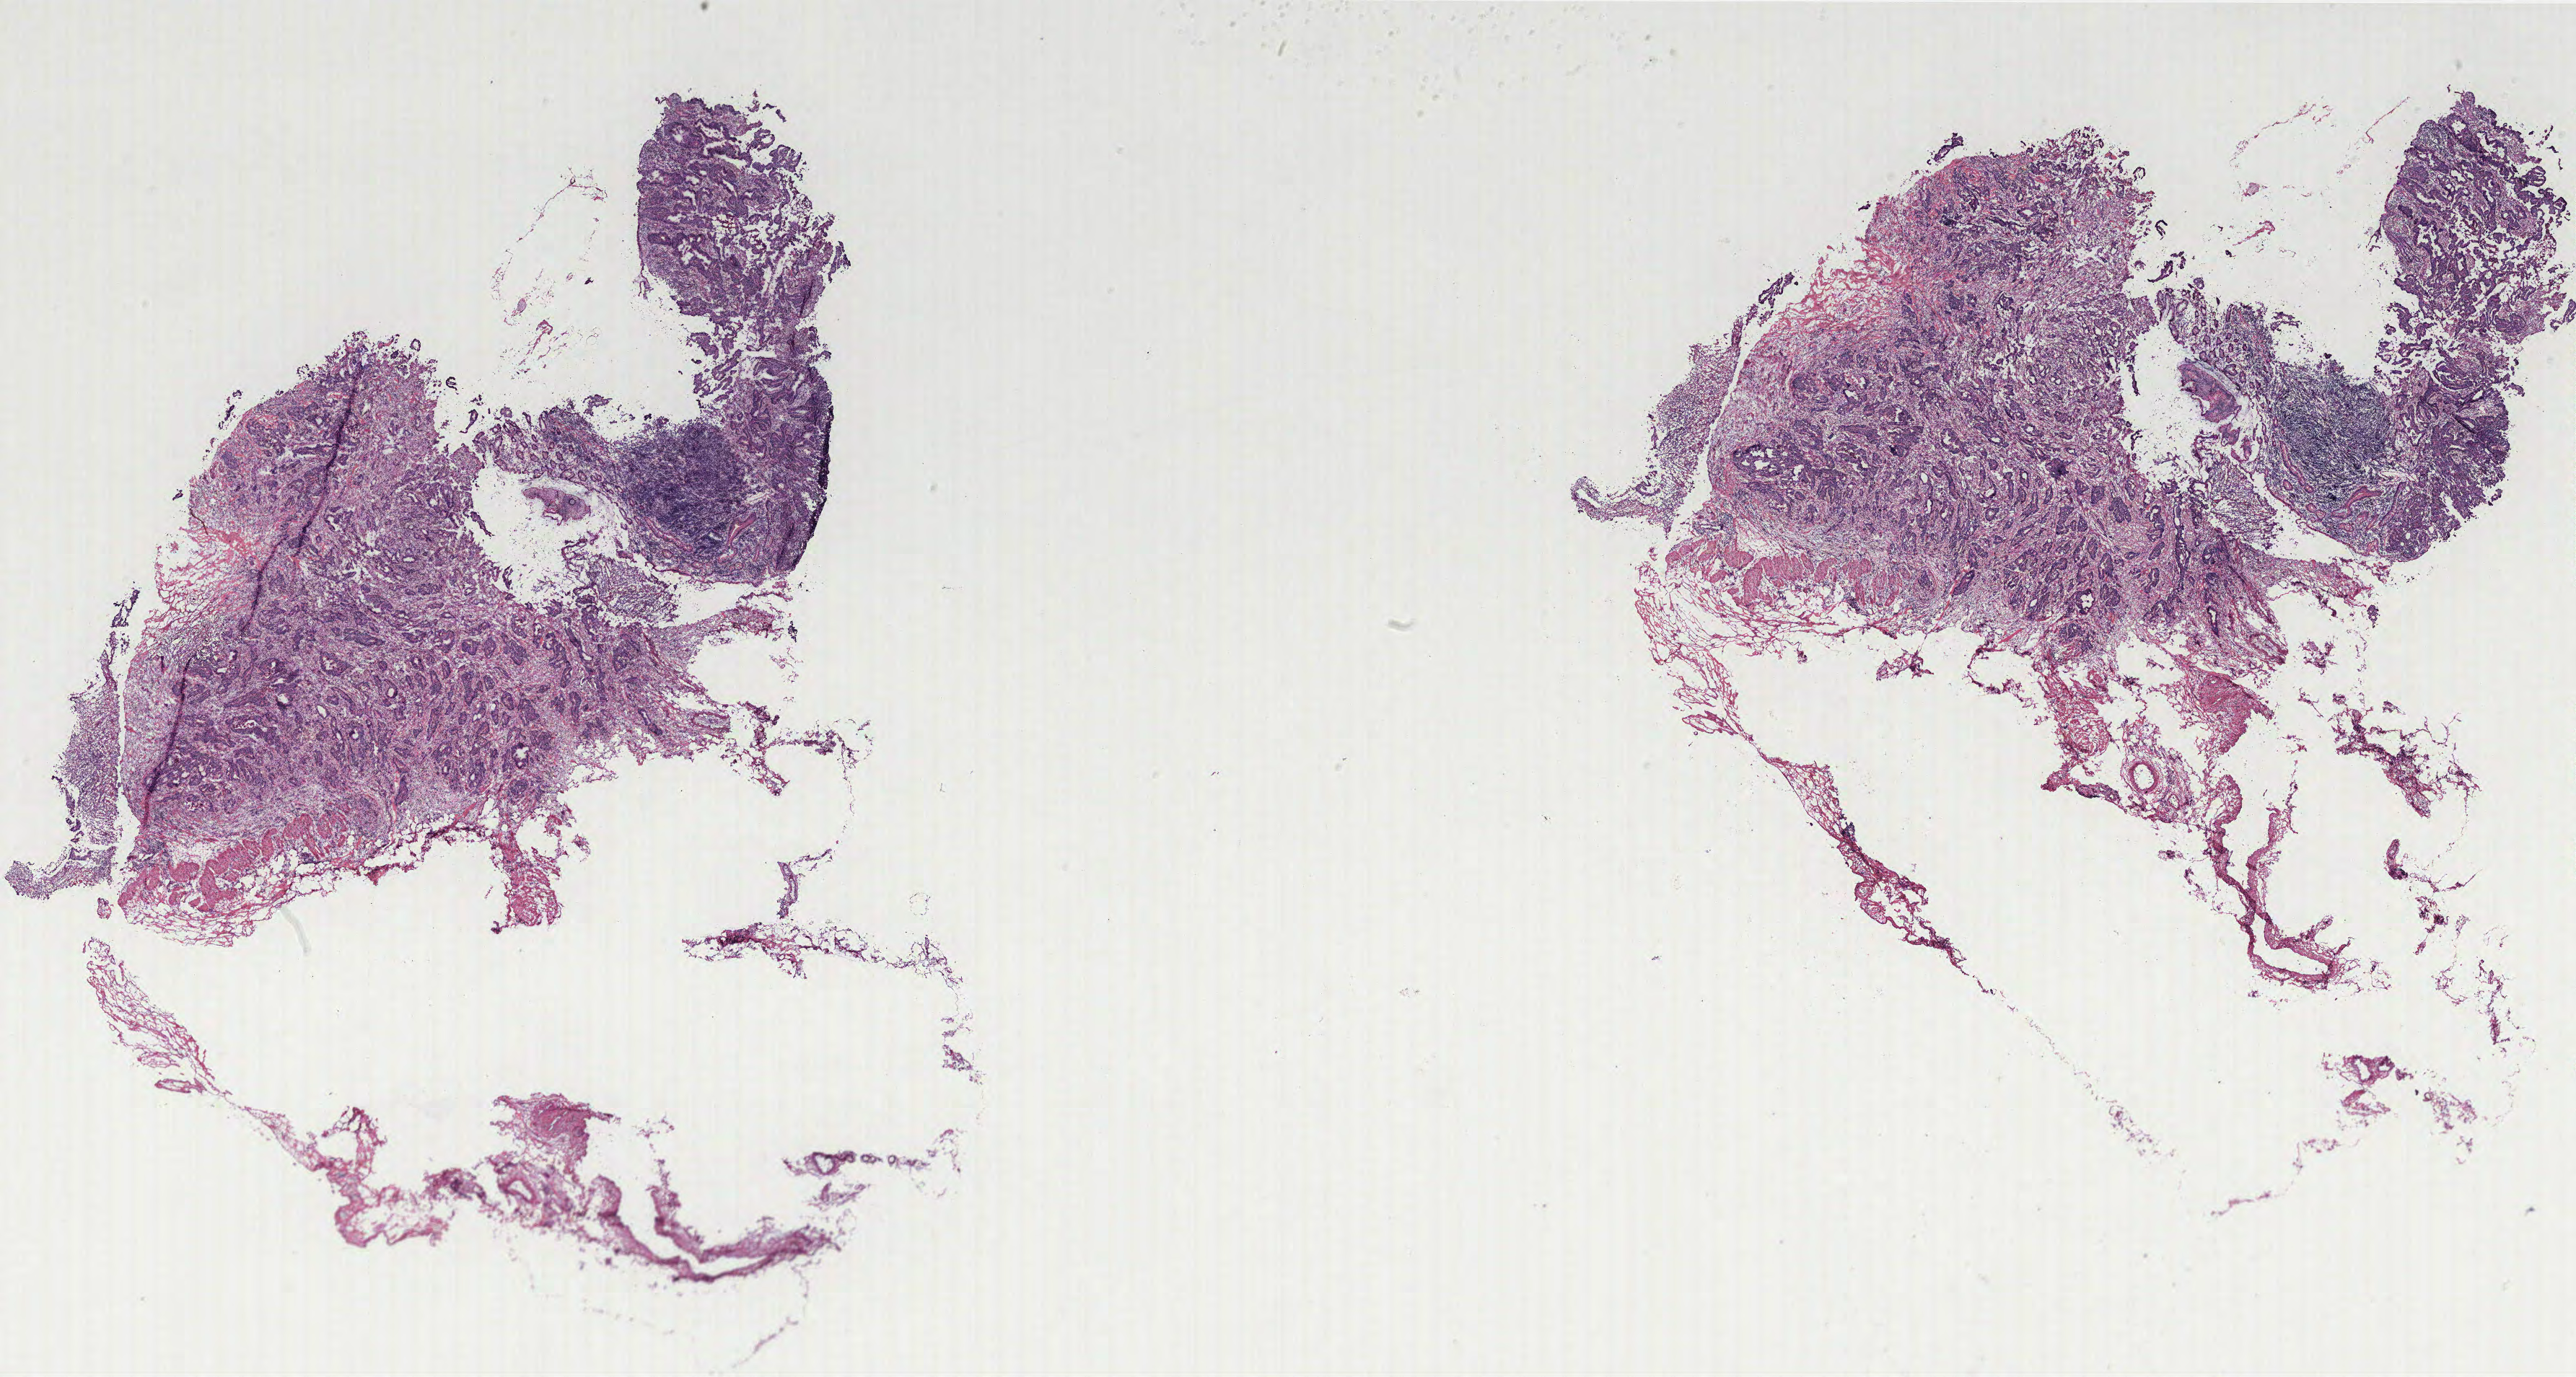
Digitized H&E tissue section (whole slide), low-resolution overview of the scanned area, about 28.6 x 15.3 mm. Tumour tissue sample, colon. Female, 50 y/o.
AJCC pathologic stage: IIIC. Diagnosis: Adenocarcinoma, NOS. Primary tumour site (as recorded): colon.